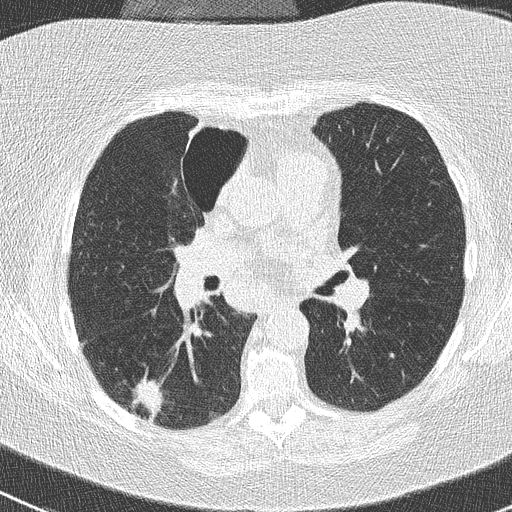
Low-dose screening chest CT, one axial slice; slice 144 of 261 in the series (ordered by position); lung window (W 1500 / L -600 HU); 2 mm slice thickness; 512 × 512 image matrix, field of view 310 × 310 mm.
Structures marked on this image (outlined manually by an expert reader):
- lesion 1 (tumor, lower lobe of right lung): box from (x=132, y=379) to (x=164, y=421) px